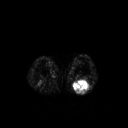
FDG PET of an extremity soft-tissue mass (from a PET/CT study), one axial slice; position 185 of 267 along the scan axis; 3.27 mm slice thickness; 128 × 128 image matrix, field of view 500 × 500 mm. Patient: male, 54 years. Case-level facts recorded for this patient, not image findings: histological type: synovial sarcoma; site of the primary tumour: left poplietal fossa.
Structures marked on this image (expert contour drawn on MRI and transferred to this co-registered scan by the dataset authors):
- gross tumour volume (mass): bounding box (x1, y1, x2, y2) in pixels: (72, 79, 91, 94)